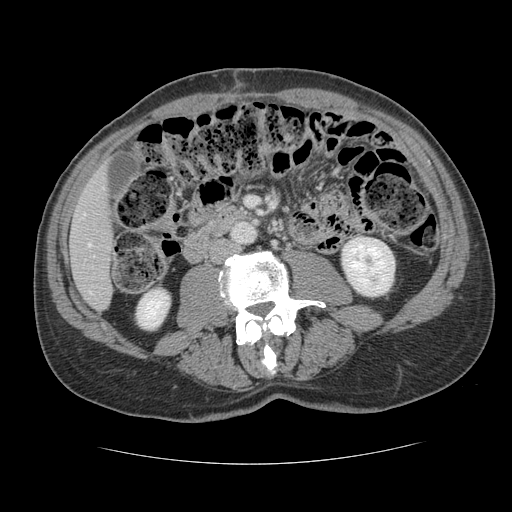
Contrast-enhanced abdominal CT, one axial slice. Slice 34 of 134 in the series (ordered by position). Reconstruction kernel STANDARD. 120 kVp. Intravenous contrast given. Soft-tissue window (W 400 / L 40 HU). 2.5 mm slice thickness. 512 × 512 image matrix, field of view 377 × 377 mm. Male patient, age 68 years. From the clinical record (not read from this slice): diagnosis: colorectal cancer liver metastases, imaged before liver resection.
Structures marked on this image (outlined manually by an expert reader):
- hepatic veins: bounding box <88,243,91,246> (left, top, right, bottom; pixels)
- liver: <71,171,114,310>
- planned liver remnant (the part of the liver to remain after resection): <71,171,114,309>